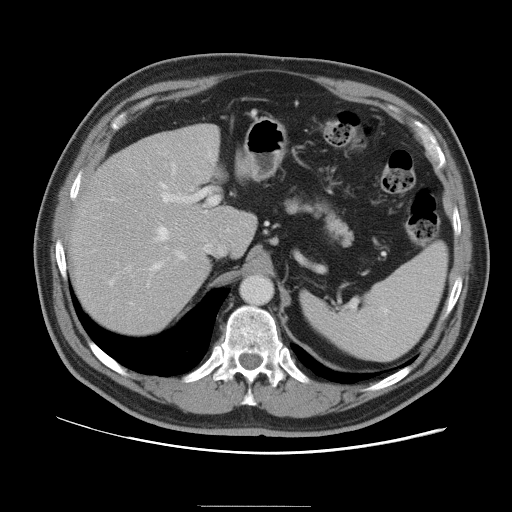
Contrast-enhanced abdominal CT, one axial slice; slice 69 of 105 in the series (ordered by position); 120 kVp; soft-tissue window (W 400 / L 40 HU); 512 × 512 image matrix. Male patient, age 64 years. Case-level facts recorded for this patient, not image findings: diagnosis: colorectal cancer liver metastases, imaged before liver resection; multiple liver metastases: yes; largest metastasis: 3 cm; disease in both lobes: yes.
Structures marked on this image (manually delineated by an expert):
- hepatic veins: bounding box (x1, y1, x2, y2) in pixels: (153, 167, 180, 269)
- liver: (70, 125, 256, 335)
- planned liver remnant (the part of the liver to remain after resection): (70, 139, 256, 336)
- portal vein (with intrahepatic branches): (109, 188, 218, 286)